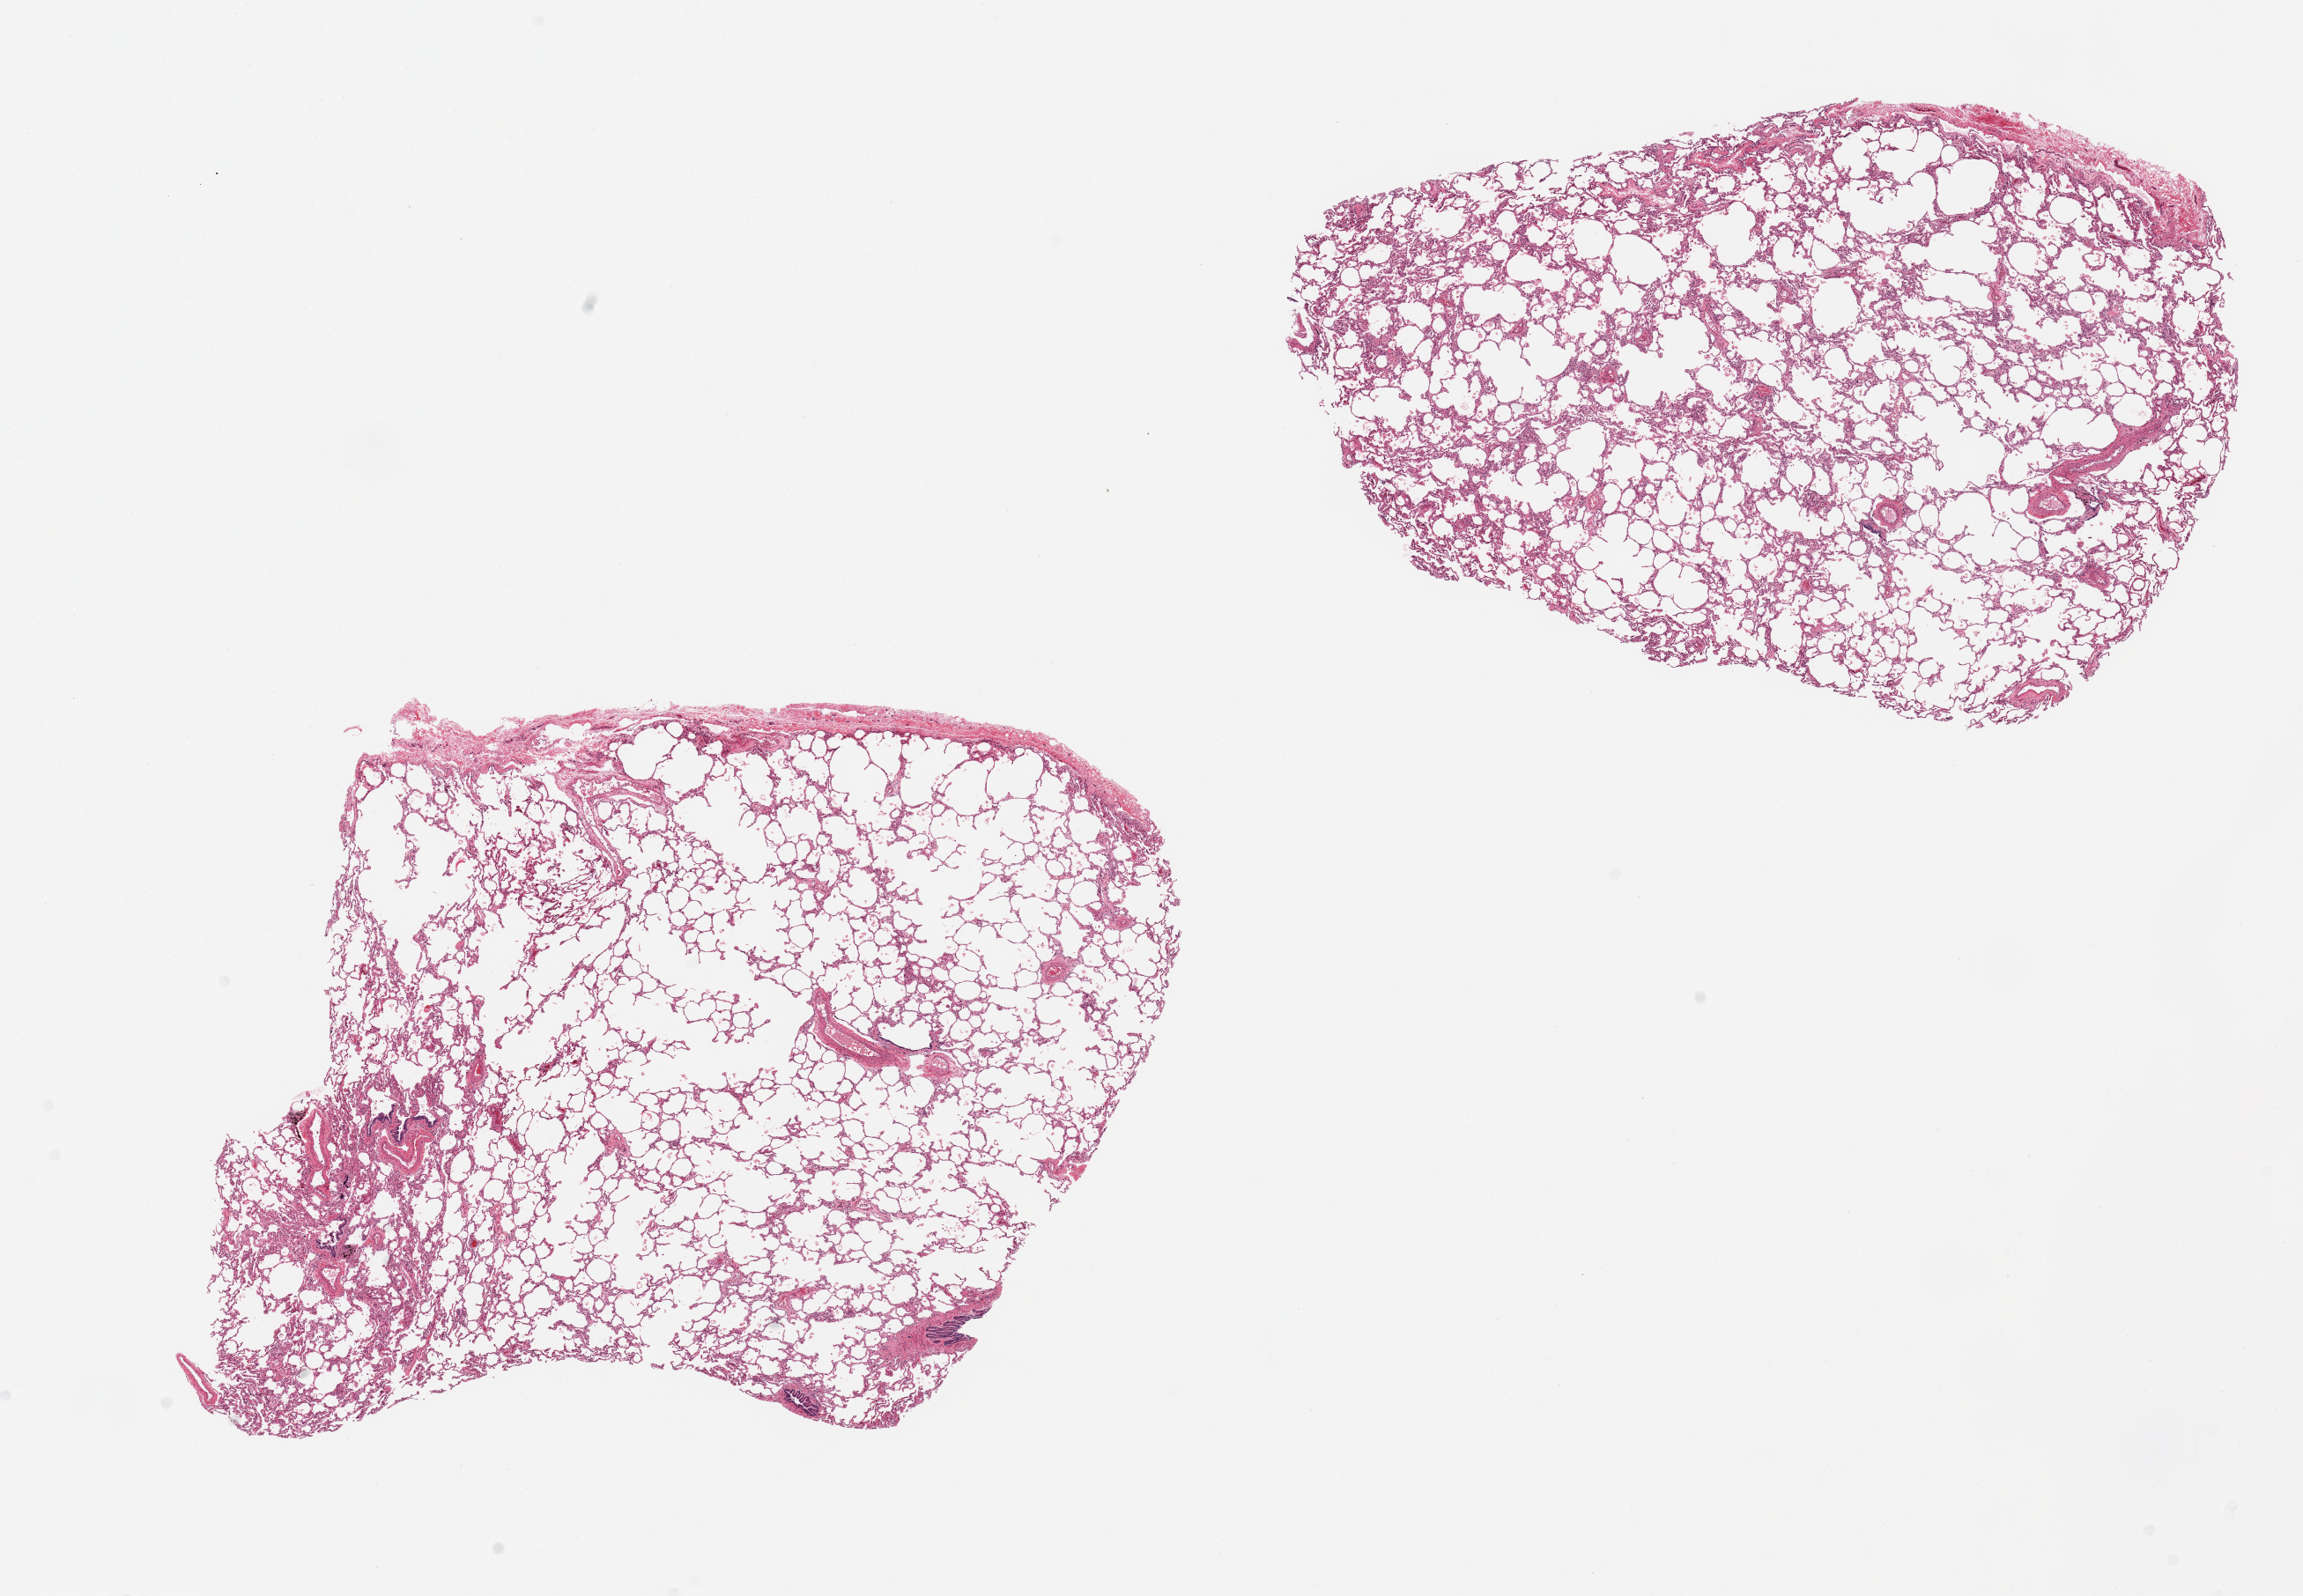
Digitized hematoxylin and eosin (H&E)-stained section, brightfield — low-resolution overview of the scanned area, about 20.7 x 14.3 mm; PAXgene-fixed, paraffin-embedded tissue; target tissue: lung; donor tissue sample. Donor: male.
Pathologist's review note for this sample: 2 pieces; distended alveolar spaces suggestive of emphysema.